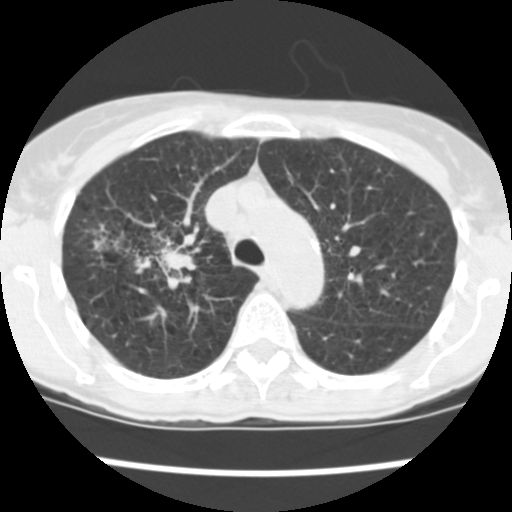
Low-dose screening chest CT, one axial slice. Position 179 of 252 along the scan axis. Reconstruction kernel STANDARD. Lung window (W 1500 / L -600 HU). 2.5 mm slice thickness. 512 × 512 image matrix.
Annotated regions visible in this slice (expert manual segmentation):
- lesion 2 (tumor, lower lobe of right lung): bounding box (x1, y1, x2, y2) in pixels: (135, 245, 195, 276)